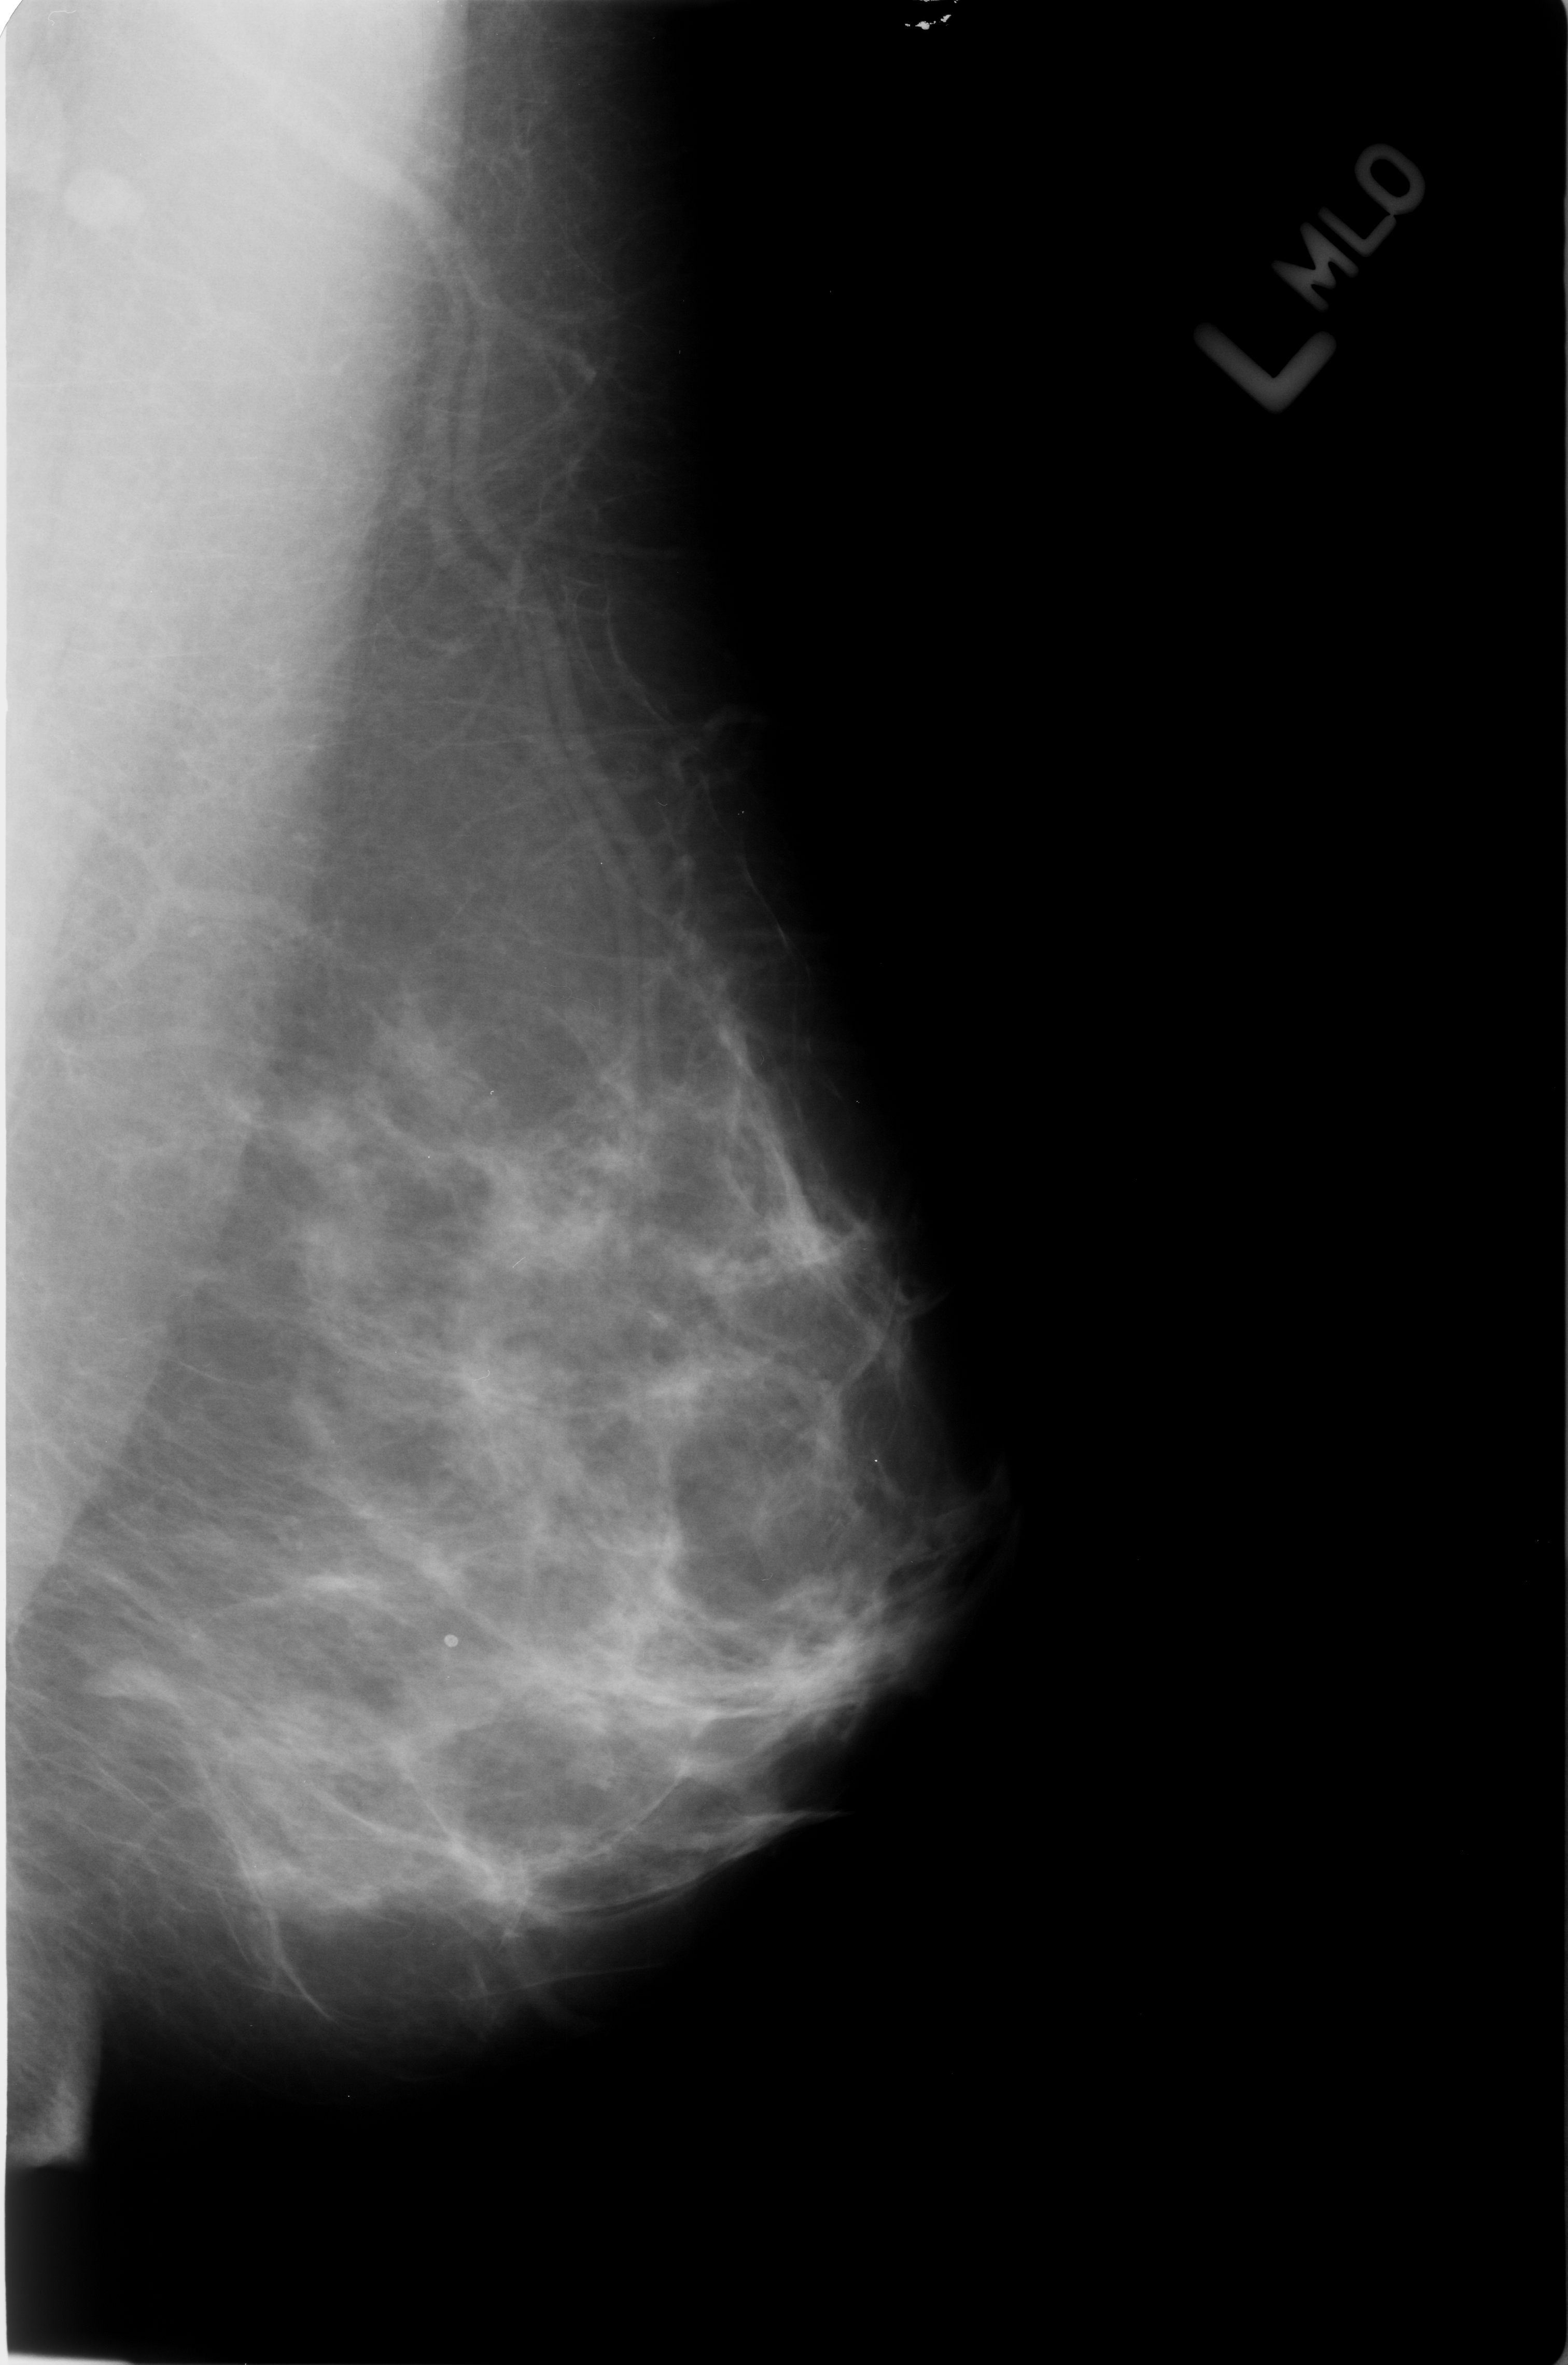
Scanned film-screen mammogram, left breast, MLO view, BI-RADS breast density category 3 (scale 1–4).
Calcifications, morphology lucent center; BI-RADS assessment category 2; benign without callback (not worked up further).